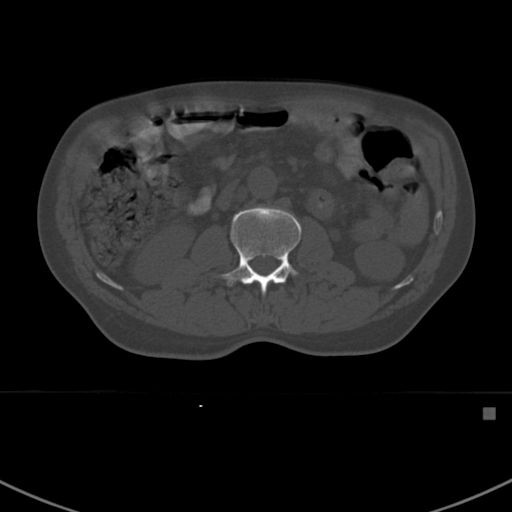
CT including the spine, one axial slice. Bone window (W 1800 / L 400 HU). 1.5 mm slice thickness. 512 × 512 image matrix. Male patient, age 59 years. From the clinical record (not read from this slice): primary cancer: prostate.
Annotated regions visible in this slice (semi-automatic segmentation, software-assisted and operator-edited):
- L2 vertebra: bounding box [x1, y1, x2, y2] px = [219, 206, 301, 295]